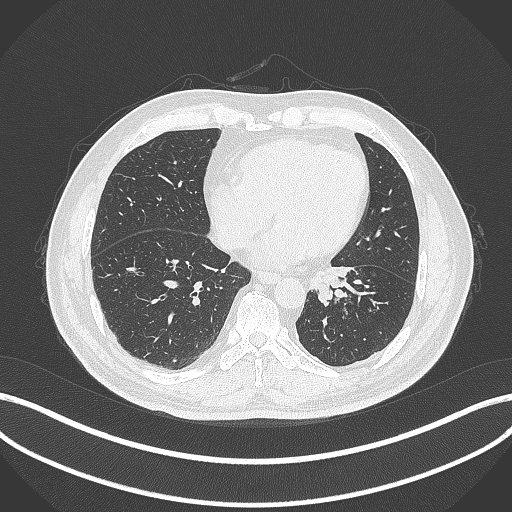
Chest CT, one axial slice. Slice 90 of 312 in the series (ordered by position). Reconstruction kernel B70f. 120 kVp. Lung window (W 1500 / L -600 HU). 512 × 512 image matrix, field of view 400 × 400 mm. Male patient, age 71 years. Case-level facts recorded for this patient, not image findings: clinical TNM (as recorded): T1b N0 M0.
Structures marked on this image (bounding box drawn by a radiologist):
- lung tumour (recorded histology: squamous cell carcinoma): bounding box <305,264,363,308> (left, top, right, bottom; pixels)